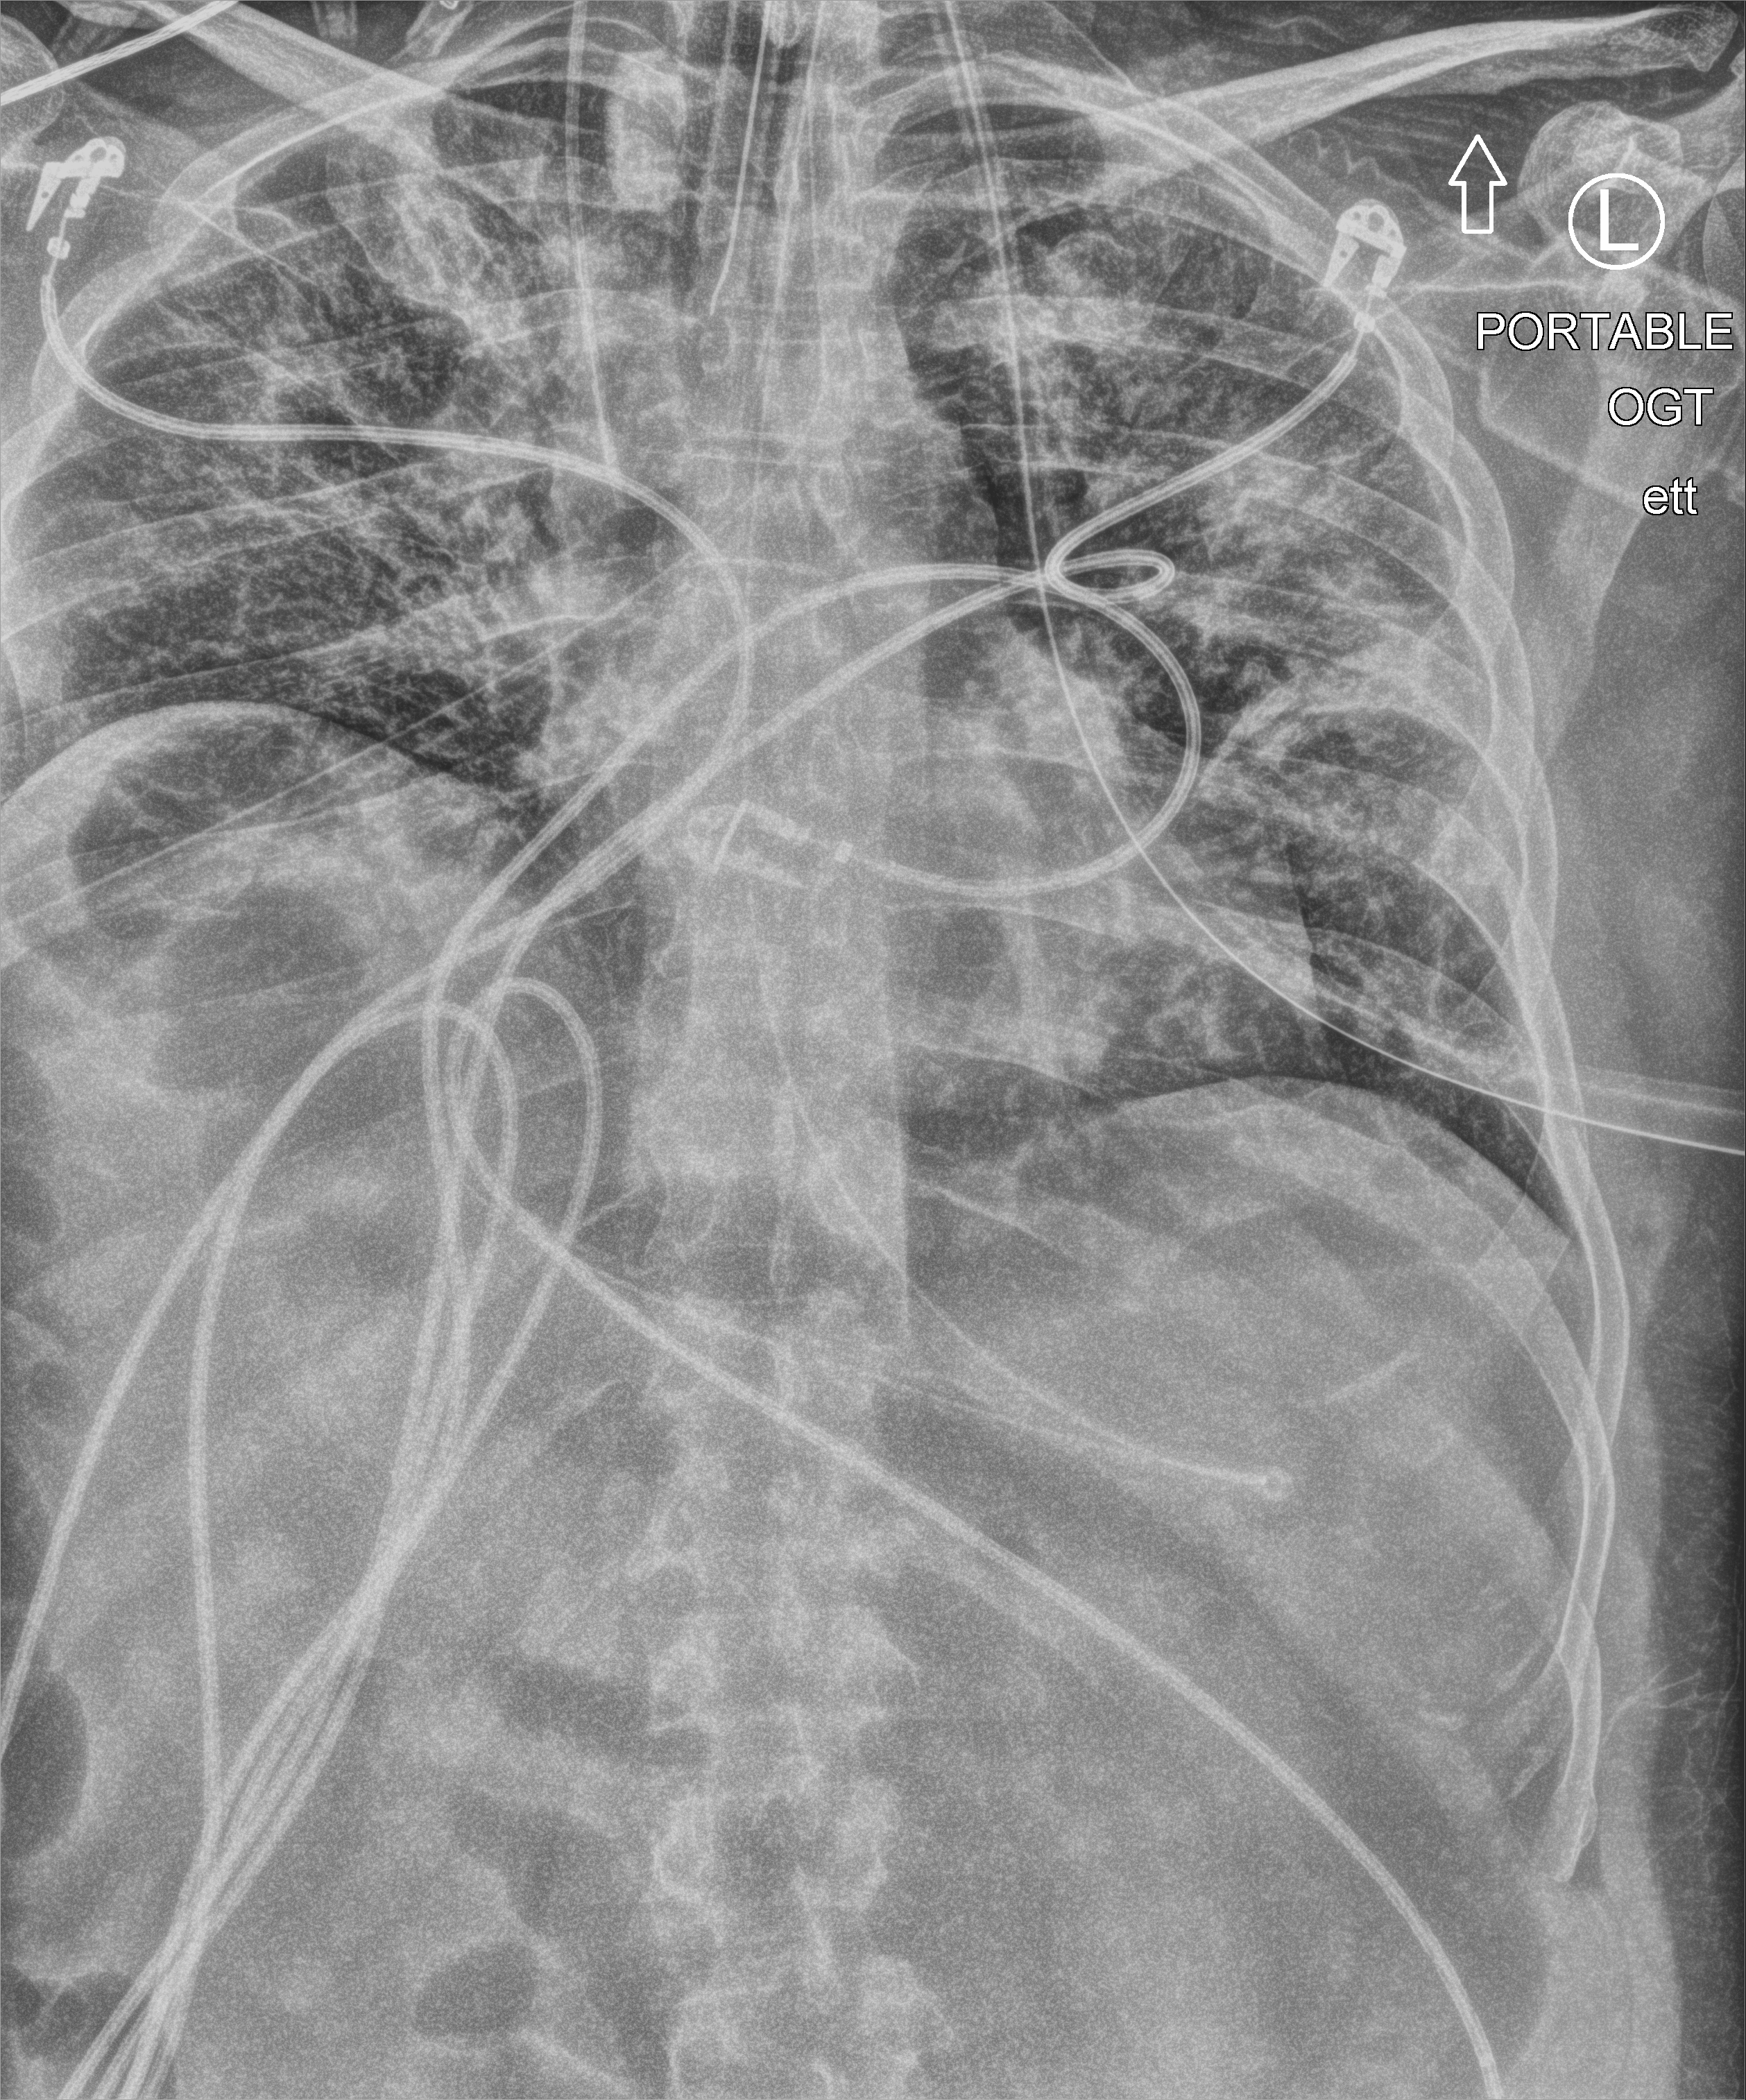
Chest X-ray (portable), anteroposterior (AP) projection. Male patient hospitalised with COVID-19, age 18–59 years.
Hospital-stay facts (about this admission, not read from this image; timing relative to this image not recorded):
- diabetes (admission record): no
- length of hospital stay: 48 days
- hypertension (admission record): no